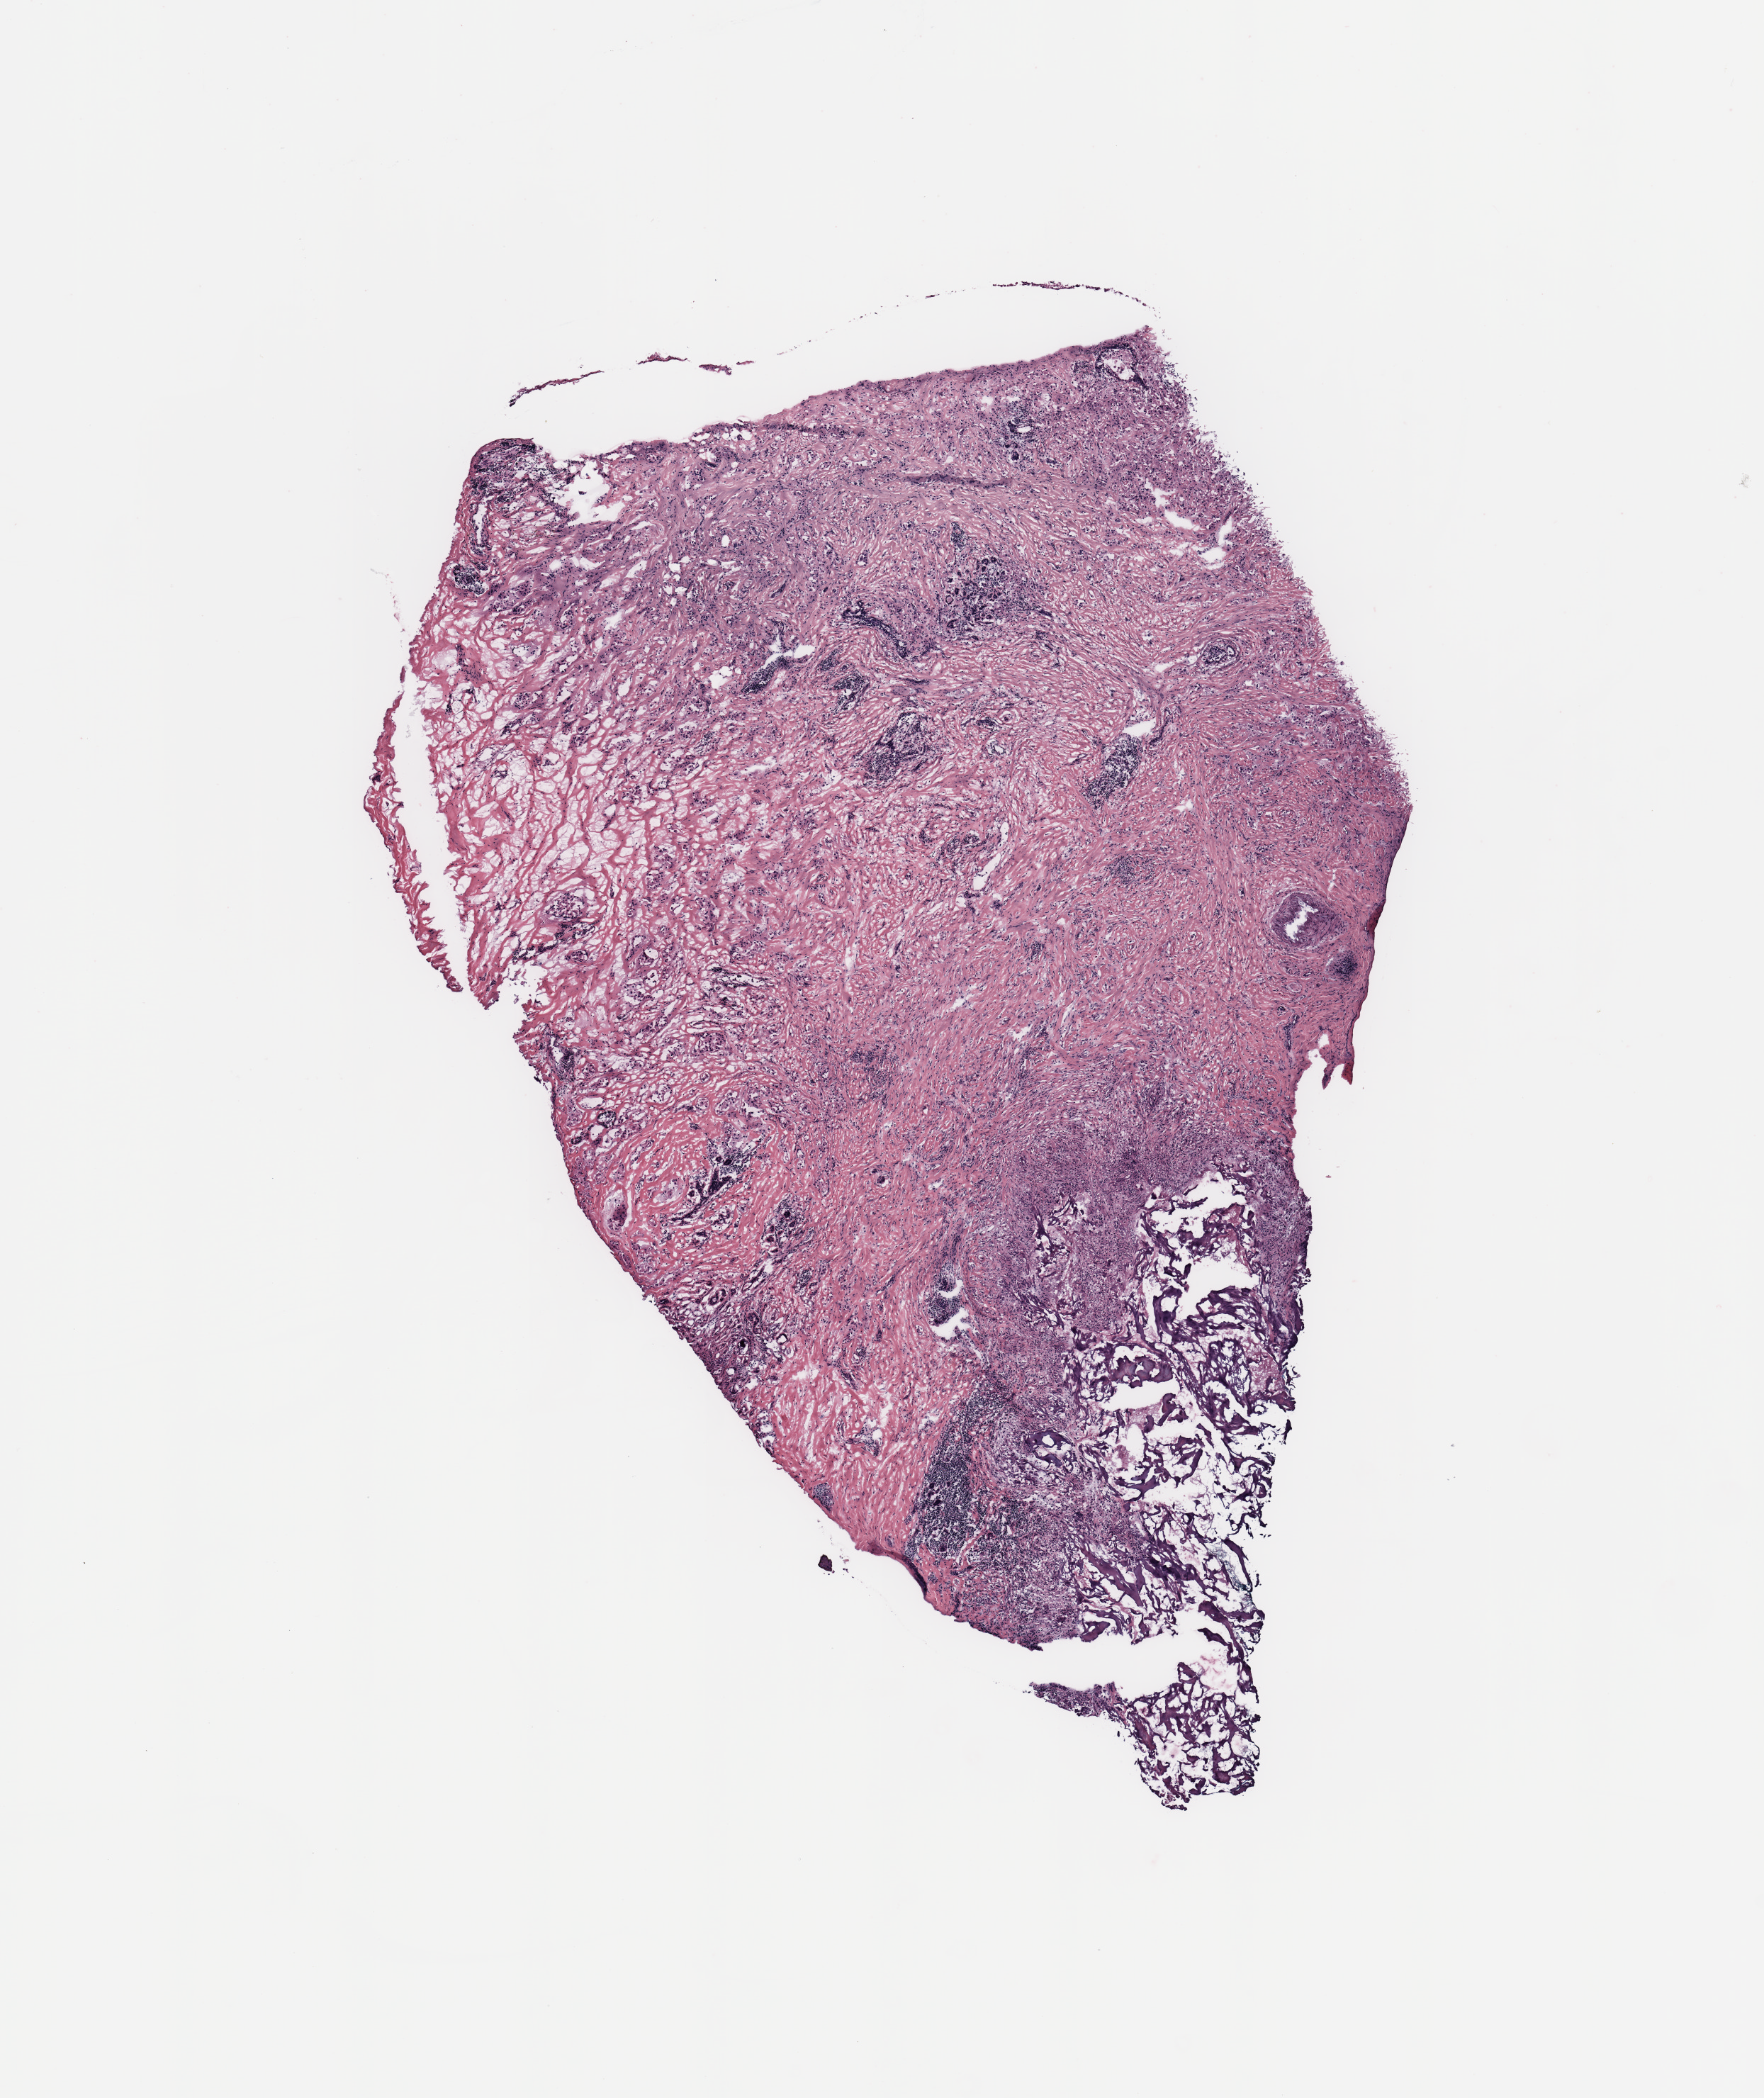
H&E whole-slide image, whole scanned area (about 9.8 x 11.7 mm) shown as a low-resolution overview. Breast, tissue type not recorded.
Patient diagnosis (cohort enrolment): breast cancer (breast).